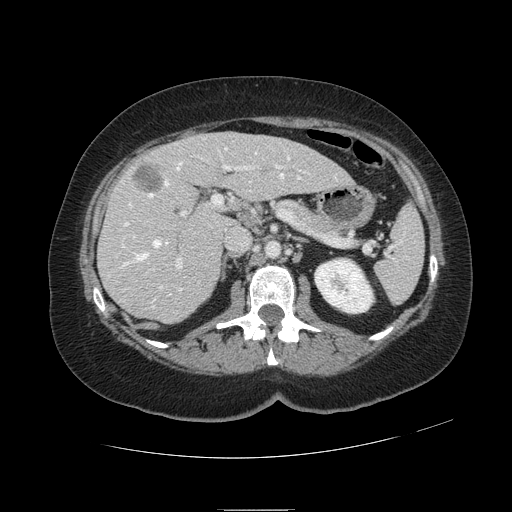
Contrast-enhanced abdominal CT, one axial slice. Slice 59 of 121 in the series (ordered by position). Intravenous contrast given. Soft-tissue window (W 400 / L 40 HU). 512 × 512 image matrix, field of view 400 × 400 mm. Female patient, age 52 years. Case-level facts recorded for this patient, not image findings: diagnosis: colorectal cancer liver metastases, imaged before liver resection; multiple liver metastases: yes; largest metastasis: 6.3 cm; chemotherapy before resection: yes.
Outlined on this slice (outlined manually by an expert reader):
- hepatic veins: bounding box [x1, y1, x2, y2] px = [123, 148, 301, 295]
- liver: [99, 133, 351, 323]
- planned liver remnant (the part of the liver to remain after resection): [168, 133, 351, 201]
- portal vein (with intrahepatic branches): [124, 165, 281, 268]
- liver metastasis: [133, 165, 162, 192]